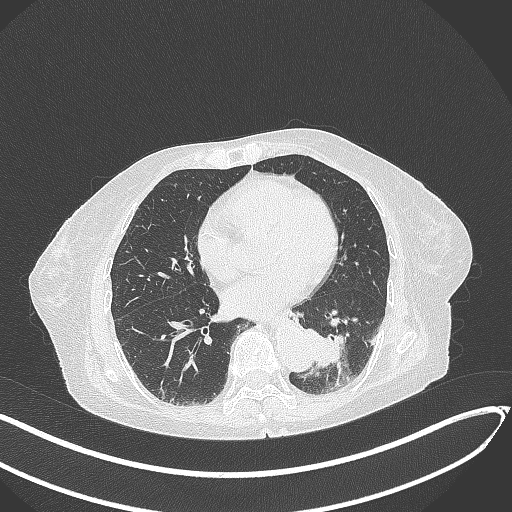
Chest CT, one axial slice. Position 98 of 324 along the scan axis. Reconstruction kernel B70f. Lung window (W 1500 / L -600 HU). 1 mm slice thickness. 512 × 512 image matrix. Patient: female, 82 years. Case-level facts recorded for this patient, not image findings: clinical TNM (as recorded): T1b N0 M1.
Structures marked on this image (bounding box drawn by a radiologist):
- lung tumour (recorded histology: adenocarcinoma): bounding box [x1, y1, x2, y2] px = [303, 325, 351, 375]